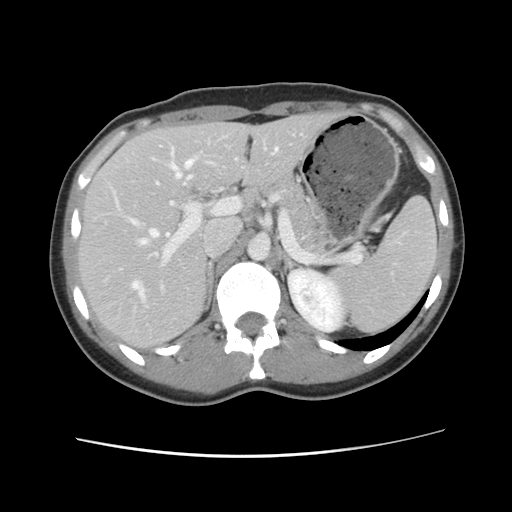
Contrast-enhanced abdominal CT, one axial slice. Slice 68 of 134 in the series (ordered by position). Soft-tissue window (W 400 / L 40 HU). 512 × 512 image matrix, field of view 339 × 339 mm. Female patient, age 33 years. Case-level facts recorded for this patient, not image findings: diagnosis: colorectal cancer liver metastases, imaged before liver resection.
Structures marked on this image (outlined manually by an expert reader):
- hepatic veins: bounding box <127,148,279,301> (left, top, right, bottom; pixels)
- liver: <79,114,335,351>
- planned liver remnant (the part of the liver to remain after resection): <79,114,336,350>
- portal vein (with intrahepatic branches): <118,141,238,292>